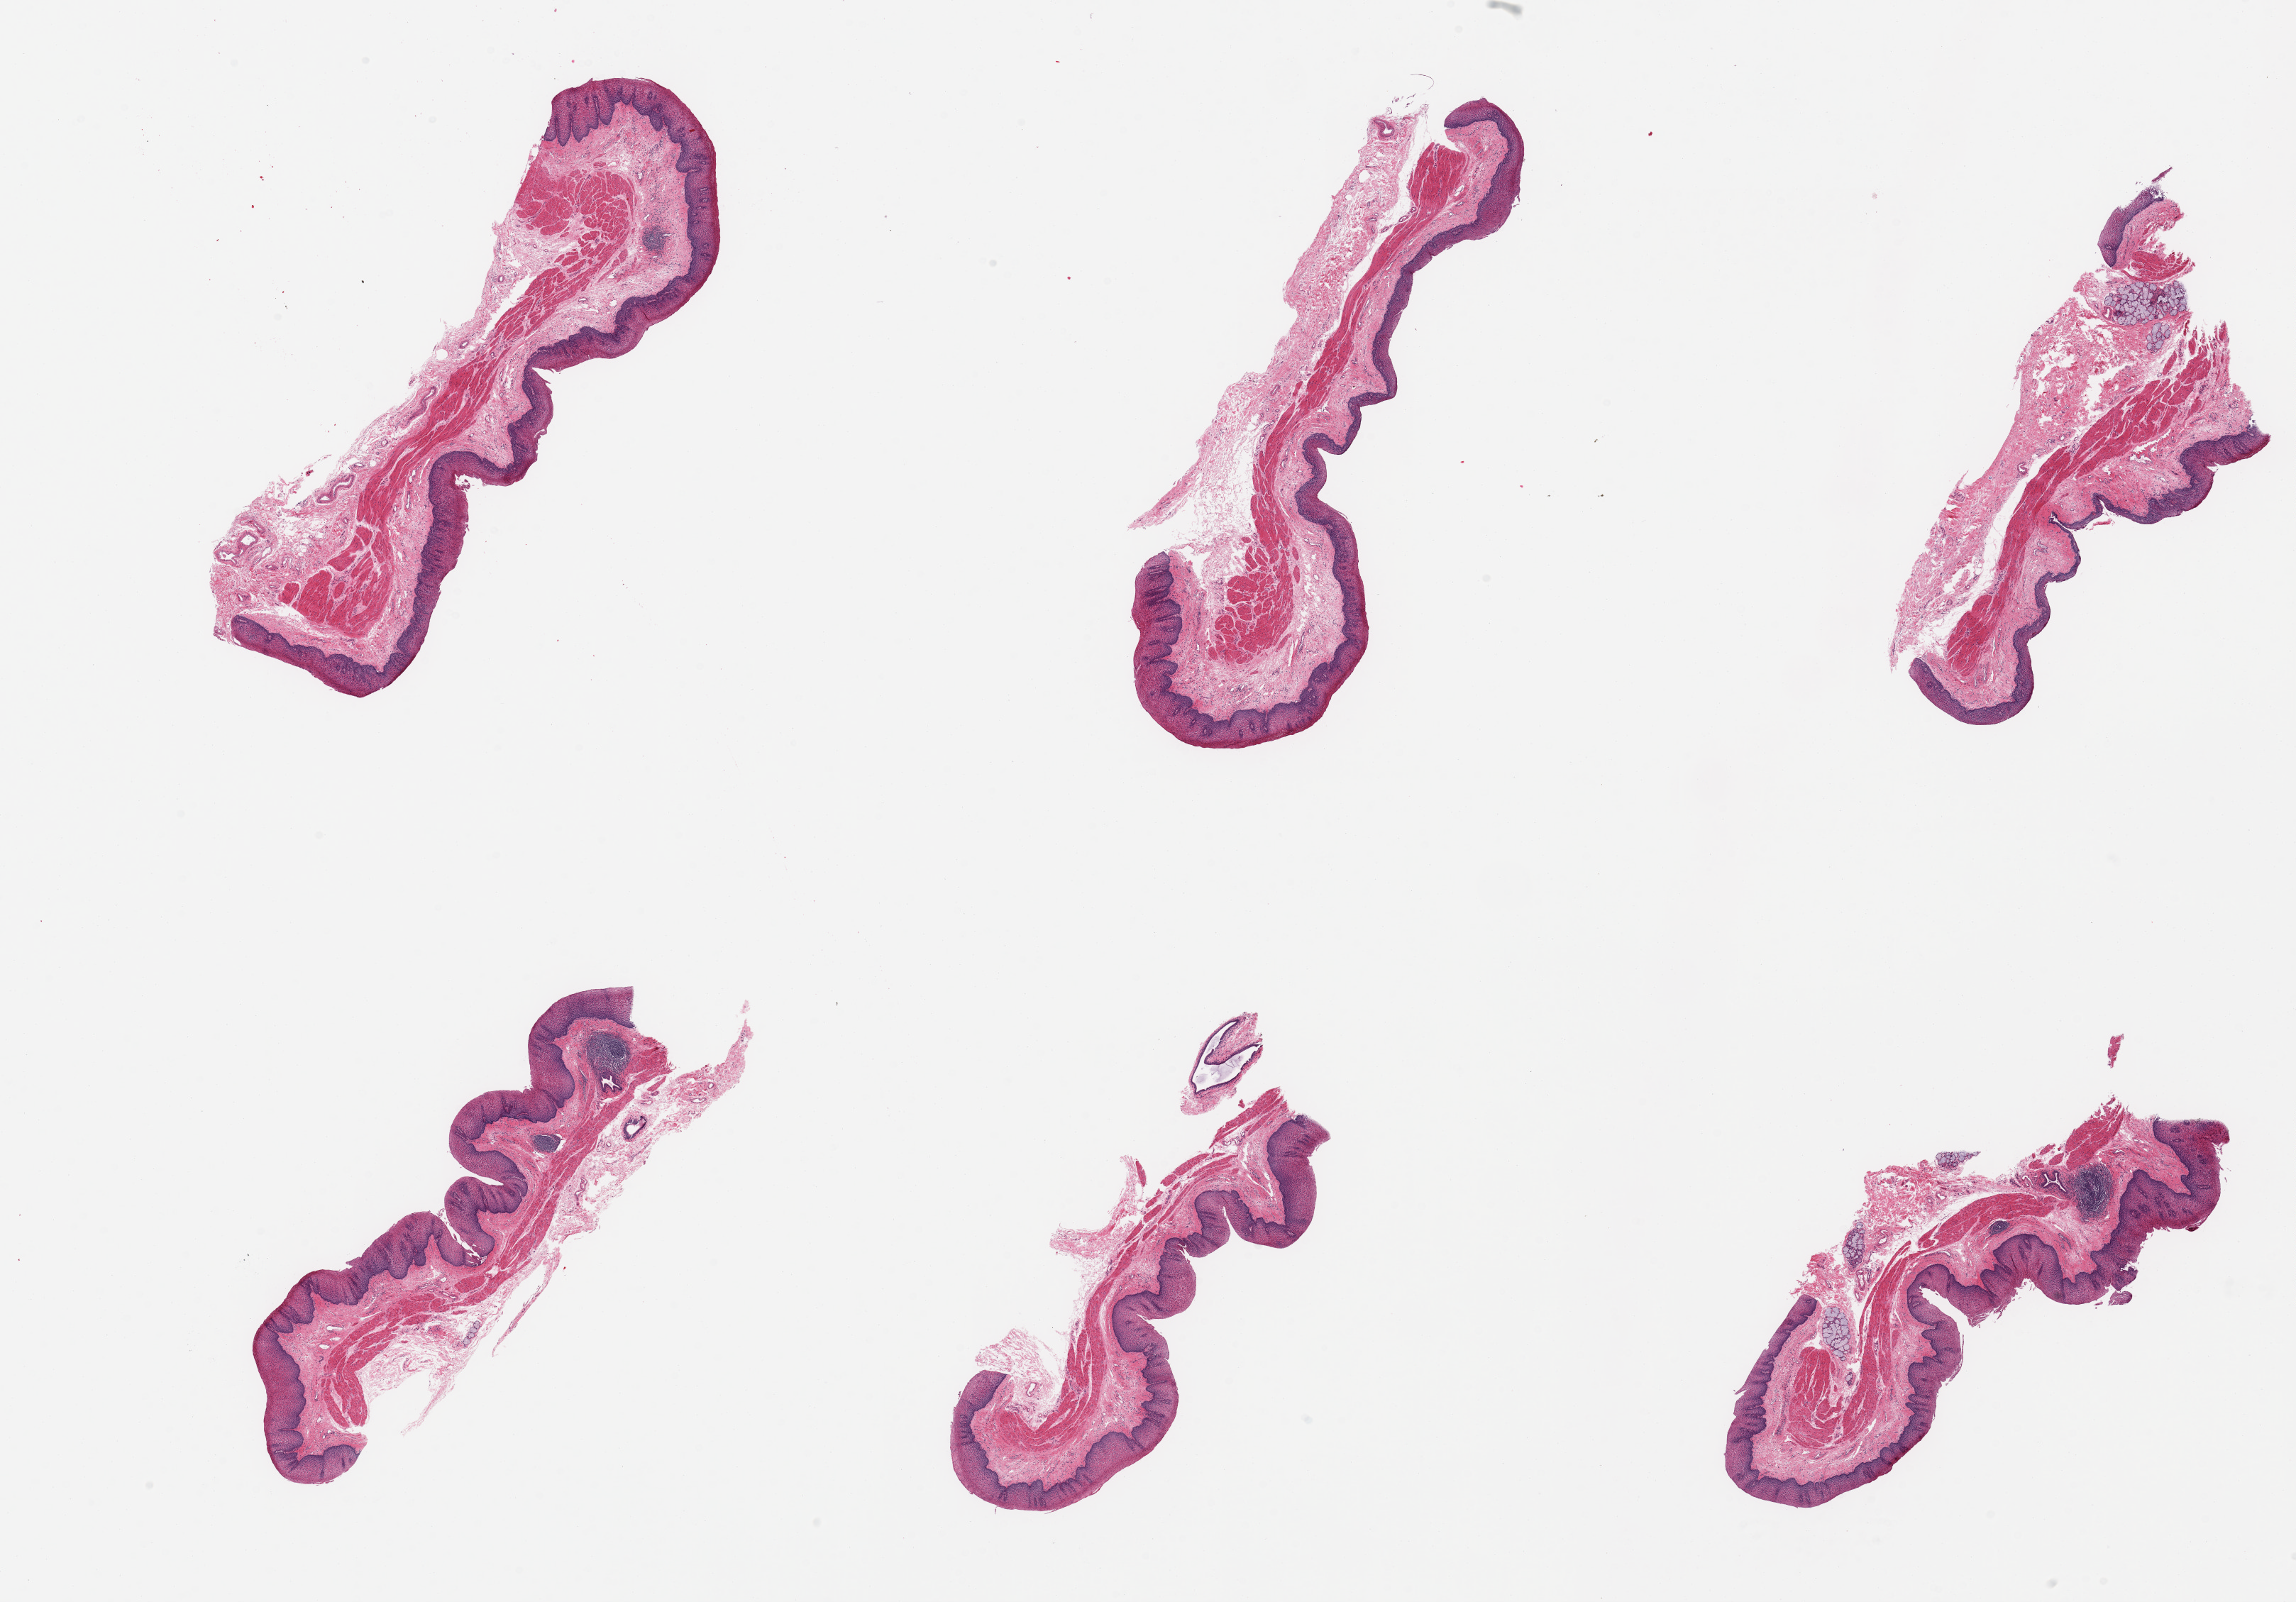
Whole-slide image, hematoxylin and eosin (H&E) stain, brightfield, a low-resolution overview of the entire scanned area, about 25.6 x 17.9 mm. PAXgene-fixed, paraffin-embedded tissue. Sampled site (target tissue): esophageal mucous membrane. Donor tissue sample. Female donor.
- review note (as recorded): 6 pieces; includes few lymphoid aggregates and clusters of submucosal glands